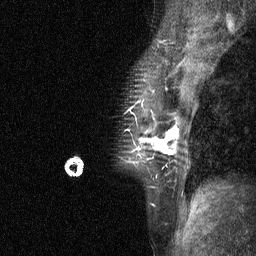
Breast MRI (dynamic contrast-enhanced), one sagittal slice; slice 44 of 64 in the series (ordered by position); dynamic contrast-enhanced study with each time point stored as its own series, time point 3 of 4 at this slice position (ordered by acquisition time); 1.5 T; TE 4.8 ms, TR 27 ms; 256 × 256 image matrix, field of view 180 × 180 mm. Patient: female, 44 years. Case-level facts recorded for this patient, not image findings: setting: breast cancer imaged before/during neoadjuvant chemotherapy; receptor status: HR-positive, HER2-negative.
Annotated regions visible in this slice (semi-automatic segmentation, software-assisted and operator-edited):
- analysis volume of interest (the breast-tissue region the enhancement analysis was run in; not a lesion): bounding box [x1, y1, x2, y2] px = [118, 117, 185, 188]
- tumour enhancement mask (voxels above the 90 % enhancement threshold inside the analysis volume of interest): [145, 128, 179, 155]